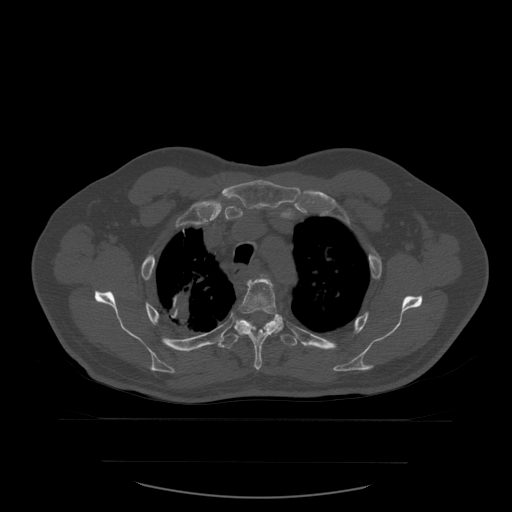
CT including the spine, one axial slice; position 438 of 590 along the scan axis; bone window (W 1800 / L 400 HU); 1.25 mm slice thickness; 512 × 512 image matrix. Patient age 71 years. Case-level facts recorded for this patient, not image findings: primary cancer: lung; vertebrae with lytic lesions (as recorded): T1, T2, L5, S1.
Structures marked on this image (semi-automatically segmented with operator editing):
- T4 vertebra: box from (x=235, y=275) to (x=284, y=370) px
- T5 vertebra: (x=218, y=319)–(x=298, y=349)